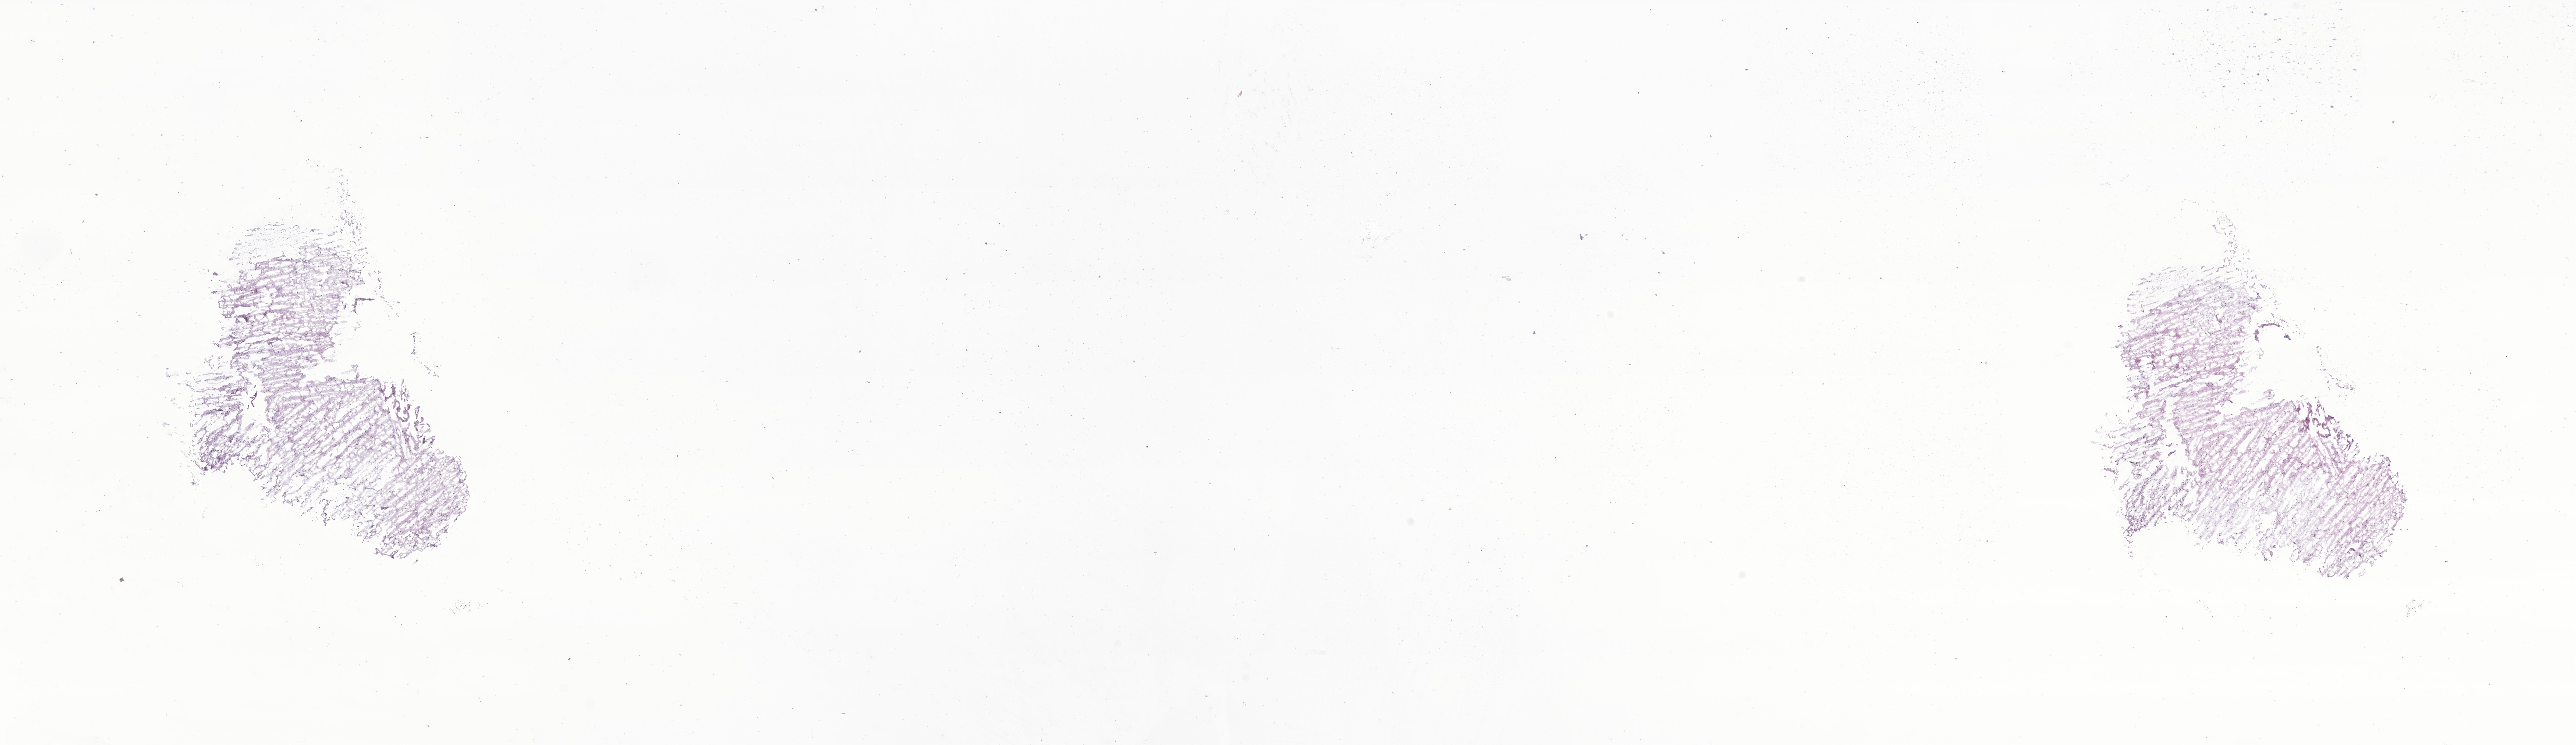
Whole-slide image, haematoxylin and eosin stain of tumor tissue from the brain — whole scanned area (about 29.5 x 8.5 mm) shown as a low-resolution overview; frozen section. Female patient, age 75 months (6 years 3 months).
• diagnosis: Pilocytic astrocytoma